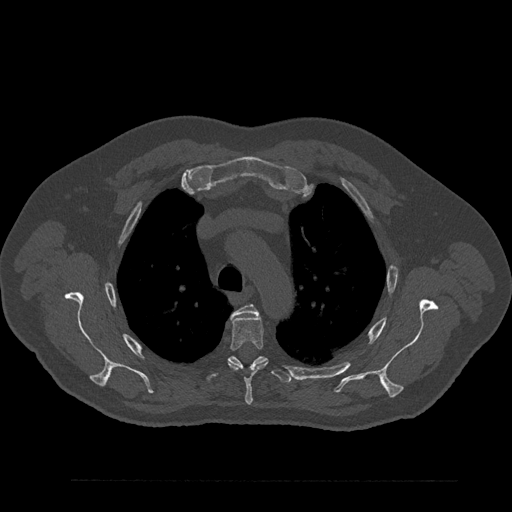
CT including the spine, one axial slice; position 634 of 797 along the scan axis; bone window (W 1800 / L 400 HU); 0.5 mm slice thickness; 512 × 512 image matrix, field of view 430 × 430 mm. Male patient, age 61 years. Case-level facts recorded for this patient, not image findings: primary cancer: prostate.
Annotated regions visible in this slice (semi-automatic segmentation, software-assisted and operator-edited):
- T3 vertebra: bounding box <231,304,258,317> (left, top, right, bottom; pixels)
- T4 vertebra: <228,315,268,405>
- T5 vertebra: <206,356,292,383>